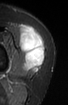
MRI of an extremity soft-tissue mass, one axial slice; slice 34 of 52 in the series (ordered by position); STIR; MR volume resampled by the dataset authors to the PET/CT grid (not the native acquisition matrix); 3.27 mm slice thickness; 68 × 105 image matrix. Female patient. From the clinical record (not read from this slice): histological type: spindle cell suggestive of biphasic synovial sarcoma; grade: intermediate; site of the primary tumour: left knee.
Structures marked on this image (expert contour drawn on MRI and transferred to this co-registered scan by the dataset authors):
- gross tumour volume including surrounding oedema: box from (x=19, y=25) to (x=45, y=71) px
- gross tumour volume (mass): (x=19, y=25)–(x=45, y=71)